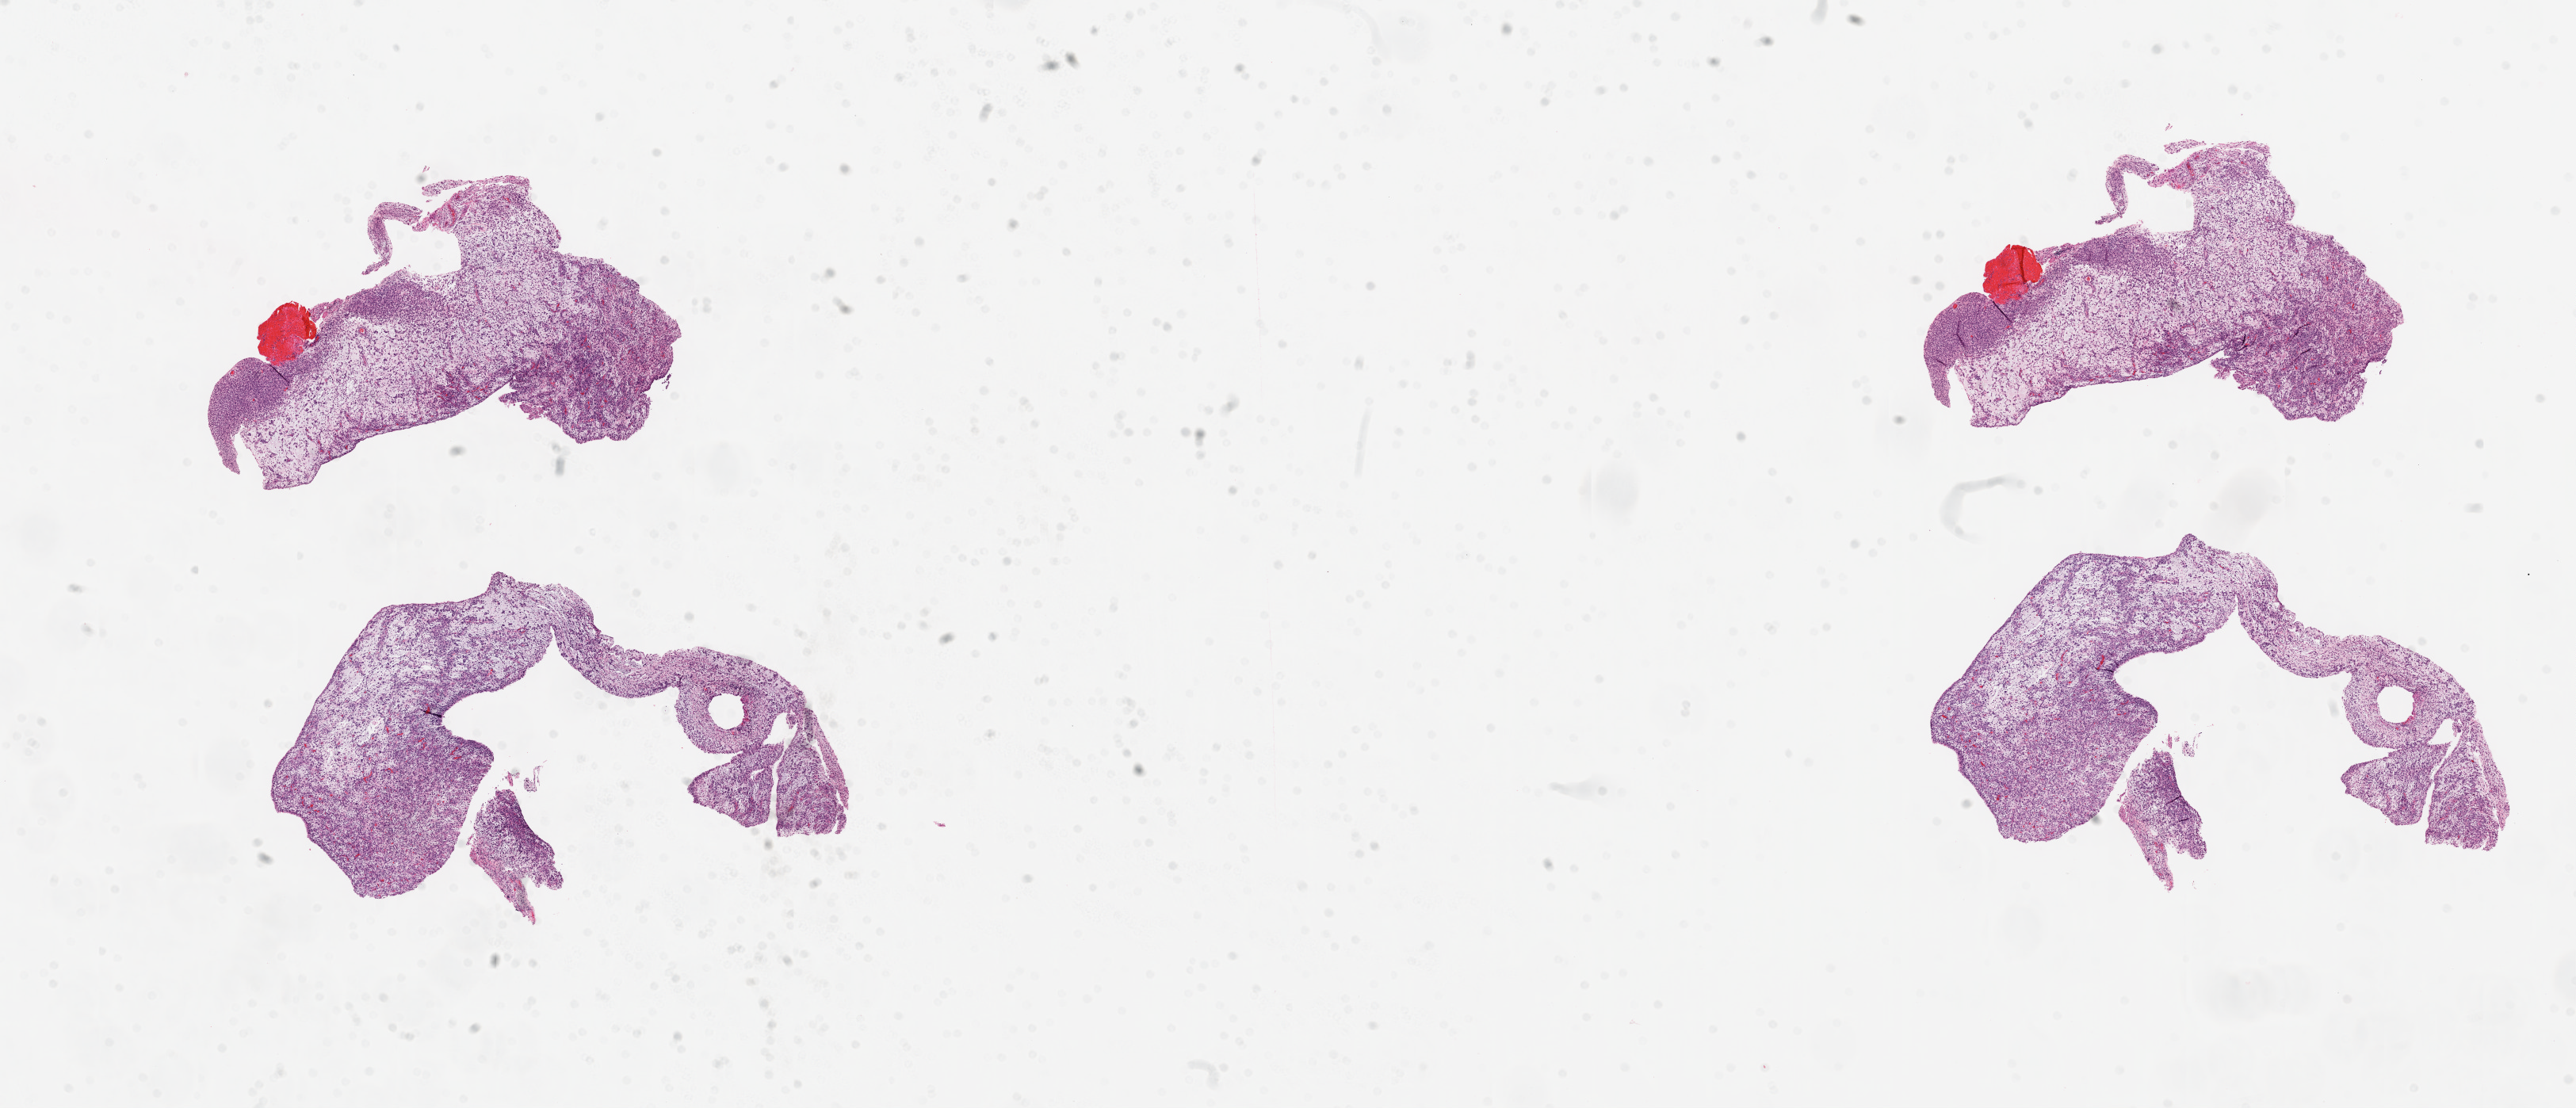
Whole-slide histology image, Hematoxylin and eosin (H&E) stained — shown as a low-resolution overview of the whole scanned area (about 26.1 x 11.2 mm, slide scanned at 20x); frozen section from the top of the tissue portion; brain, primary tumour sample. Male patient; age at initial diagnosis 63 years. Pathologist review of this section (percent, as recorded): tumour cells 85%, tumour nuclei 80%, normal cells 0%, stromal cells 15%, necrosis 0%.
• histologic diagnosis: Glioblastoma